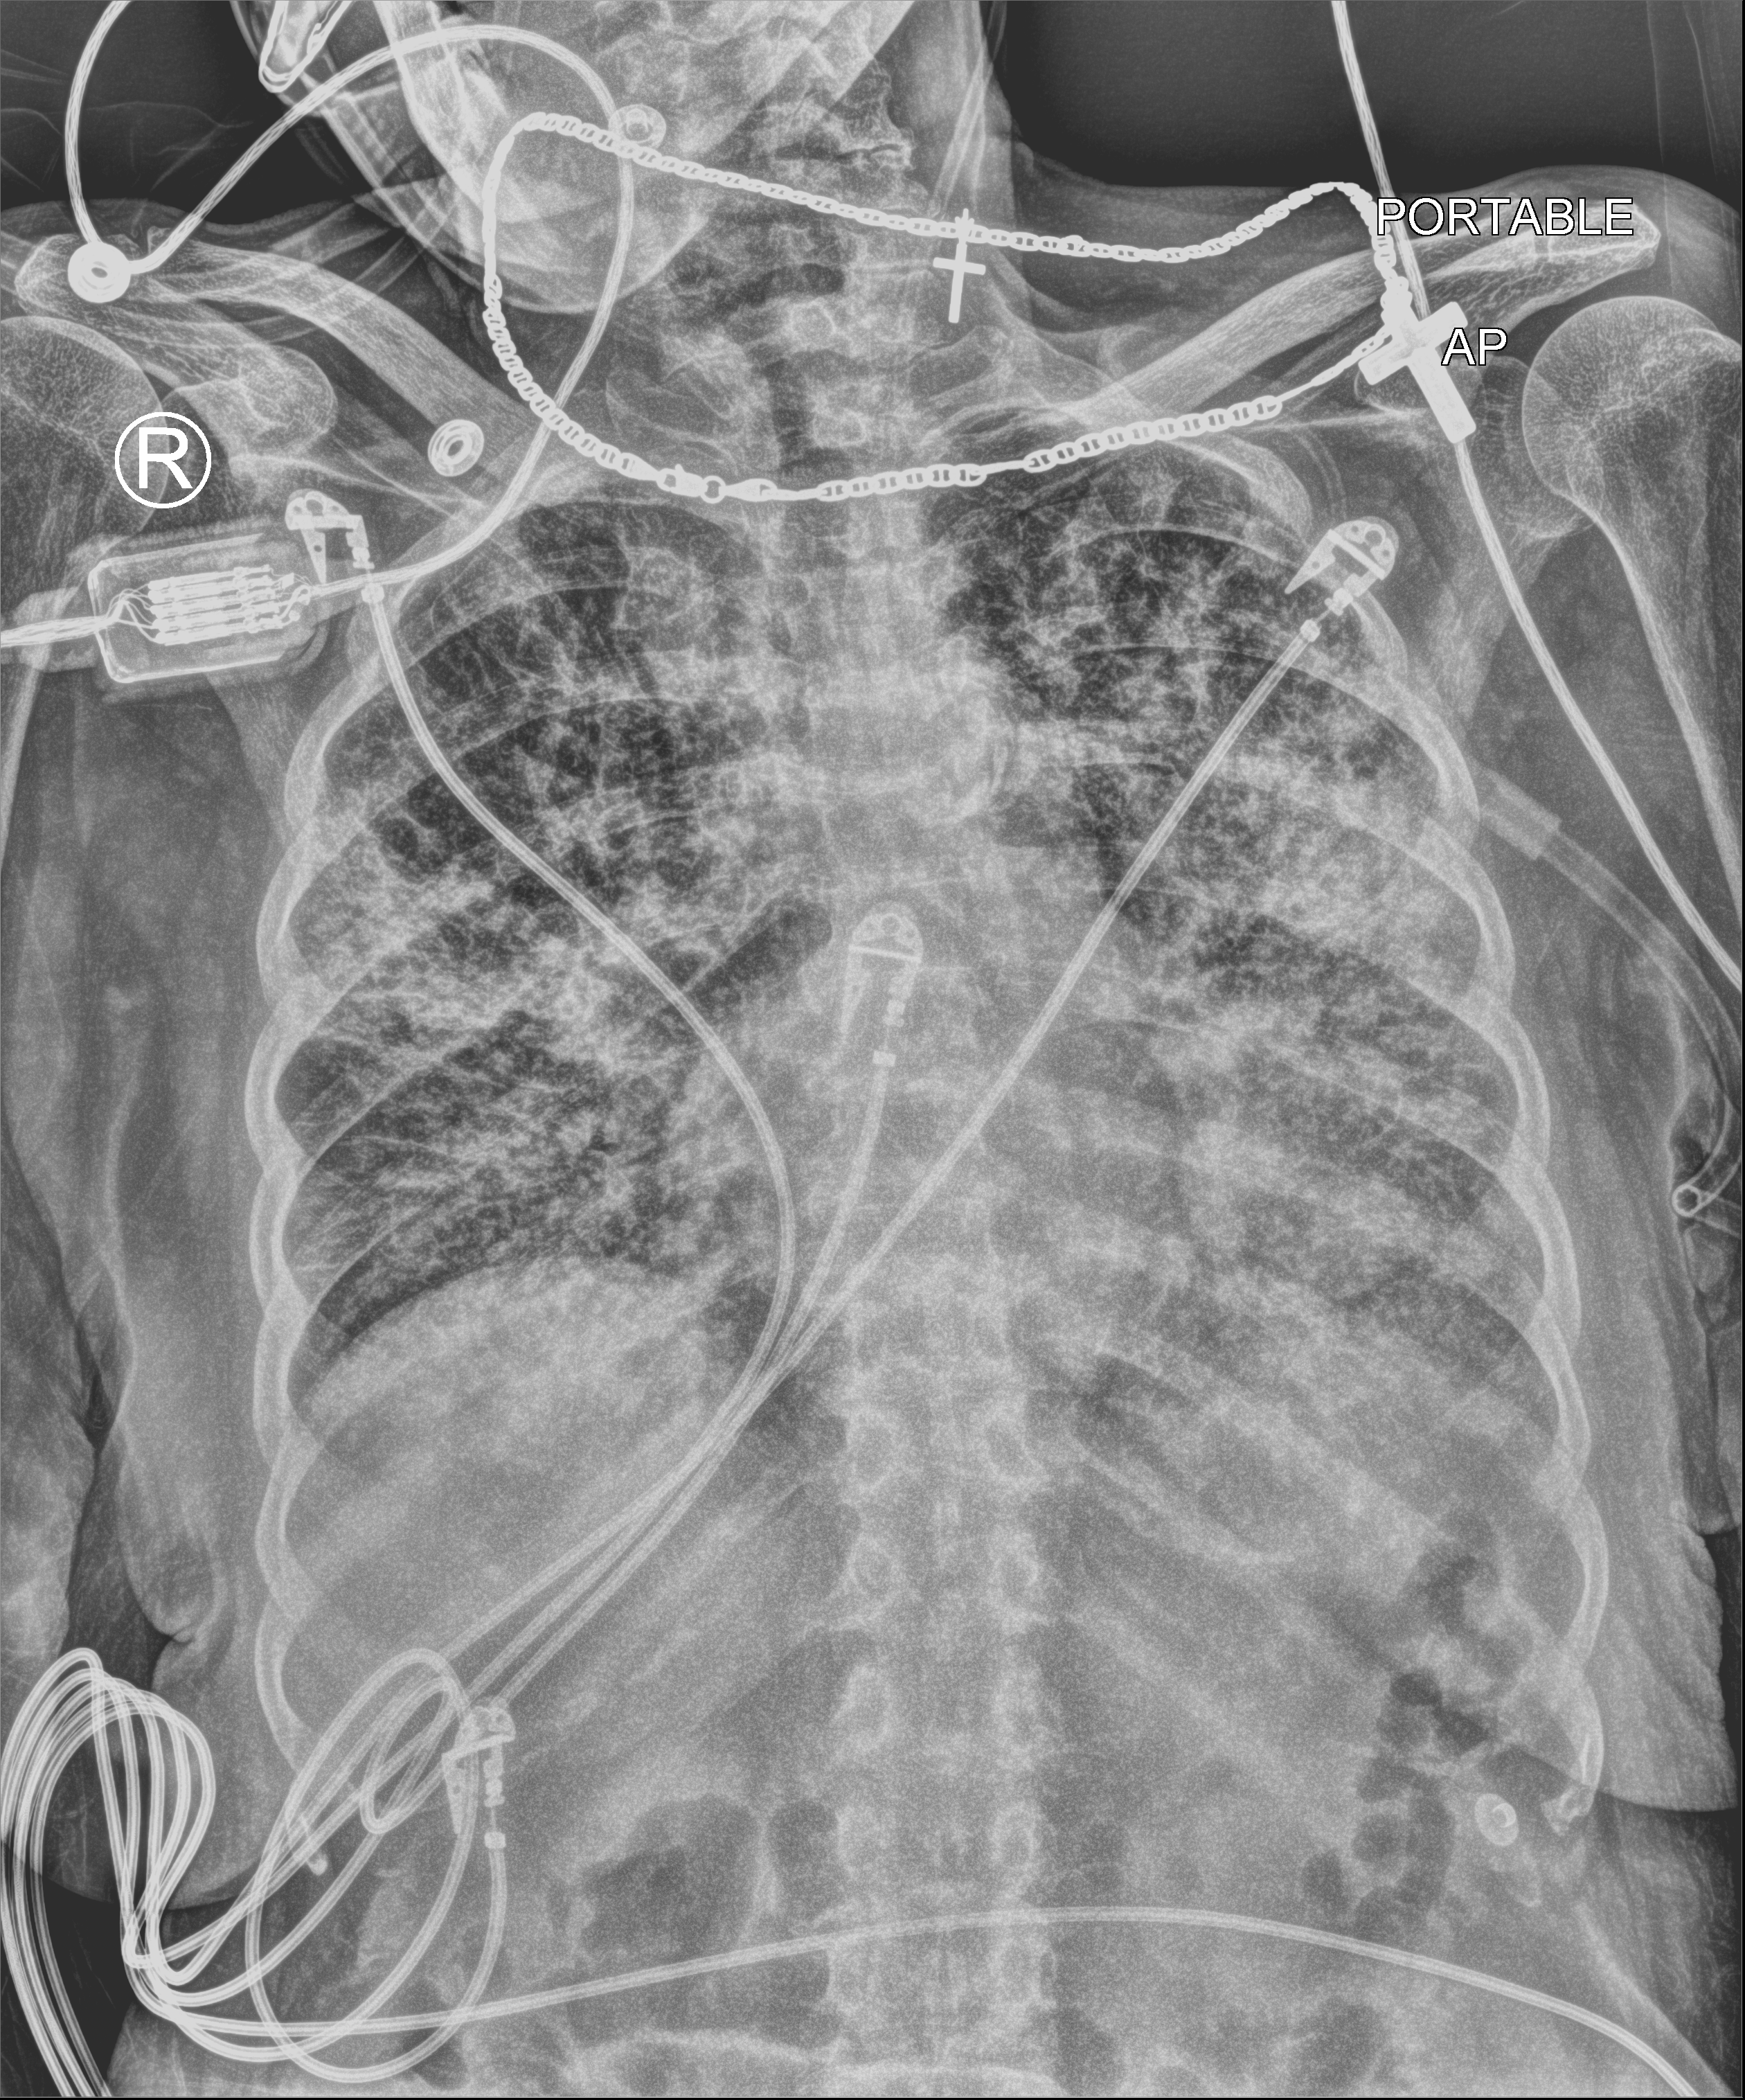
Bedside chest radiograph (computed radiography); anteroposterior (AP) projection. Patient hospitalised with COVID-19; female, aged 75–90 years.
Hospital-stay facts (about this admission, not read from this image; timing relative to this image not recorded):
- mechanically ventilated during this hospital stay: no
- admitted to intensive care during this hospital stay: no